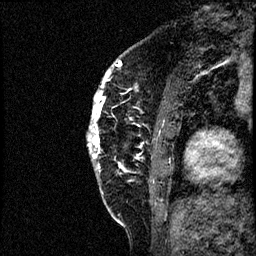
Breast MRI (dynamic contrast-enhanced), one sagittal slice. Slice 13 of 60 in the series (ordered by position). Dynamic contrast-enhanced study with each time point stored as its own series, time point 2 of 4 at this slice position (early post-contrast, ordered by acquisition time). 1.5 T. TE 4.2 ms, TR 17.6 ms. 2 mm slice thickness. 256 × 256 image matrix, field of view 200 × 200 mm. Patient: female, 40 years. Case-level facts recorded for this patient, not image findings: setting: breast cancer imaged before/during neoadjuvant chemotherapy; receptor status: HER2-positive.
Outlined on this slice (semi-automatic segmentation, software-assisted and operator-edited):
- analysis volume of interest (the breast-tissue region the enhancement analysis was run in; not a lesion): box from (x=88, y=56) to (x=197, y=205) px
- tumour enhancement mask (voxels above the 100 % enhancement threshold inside the analysis volume of interest): (x=88, y=60)–(x=160, y=181)